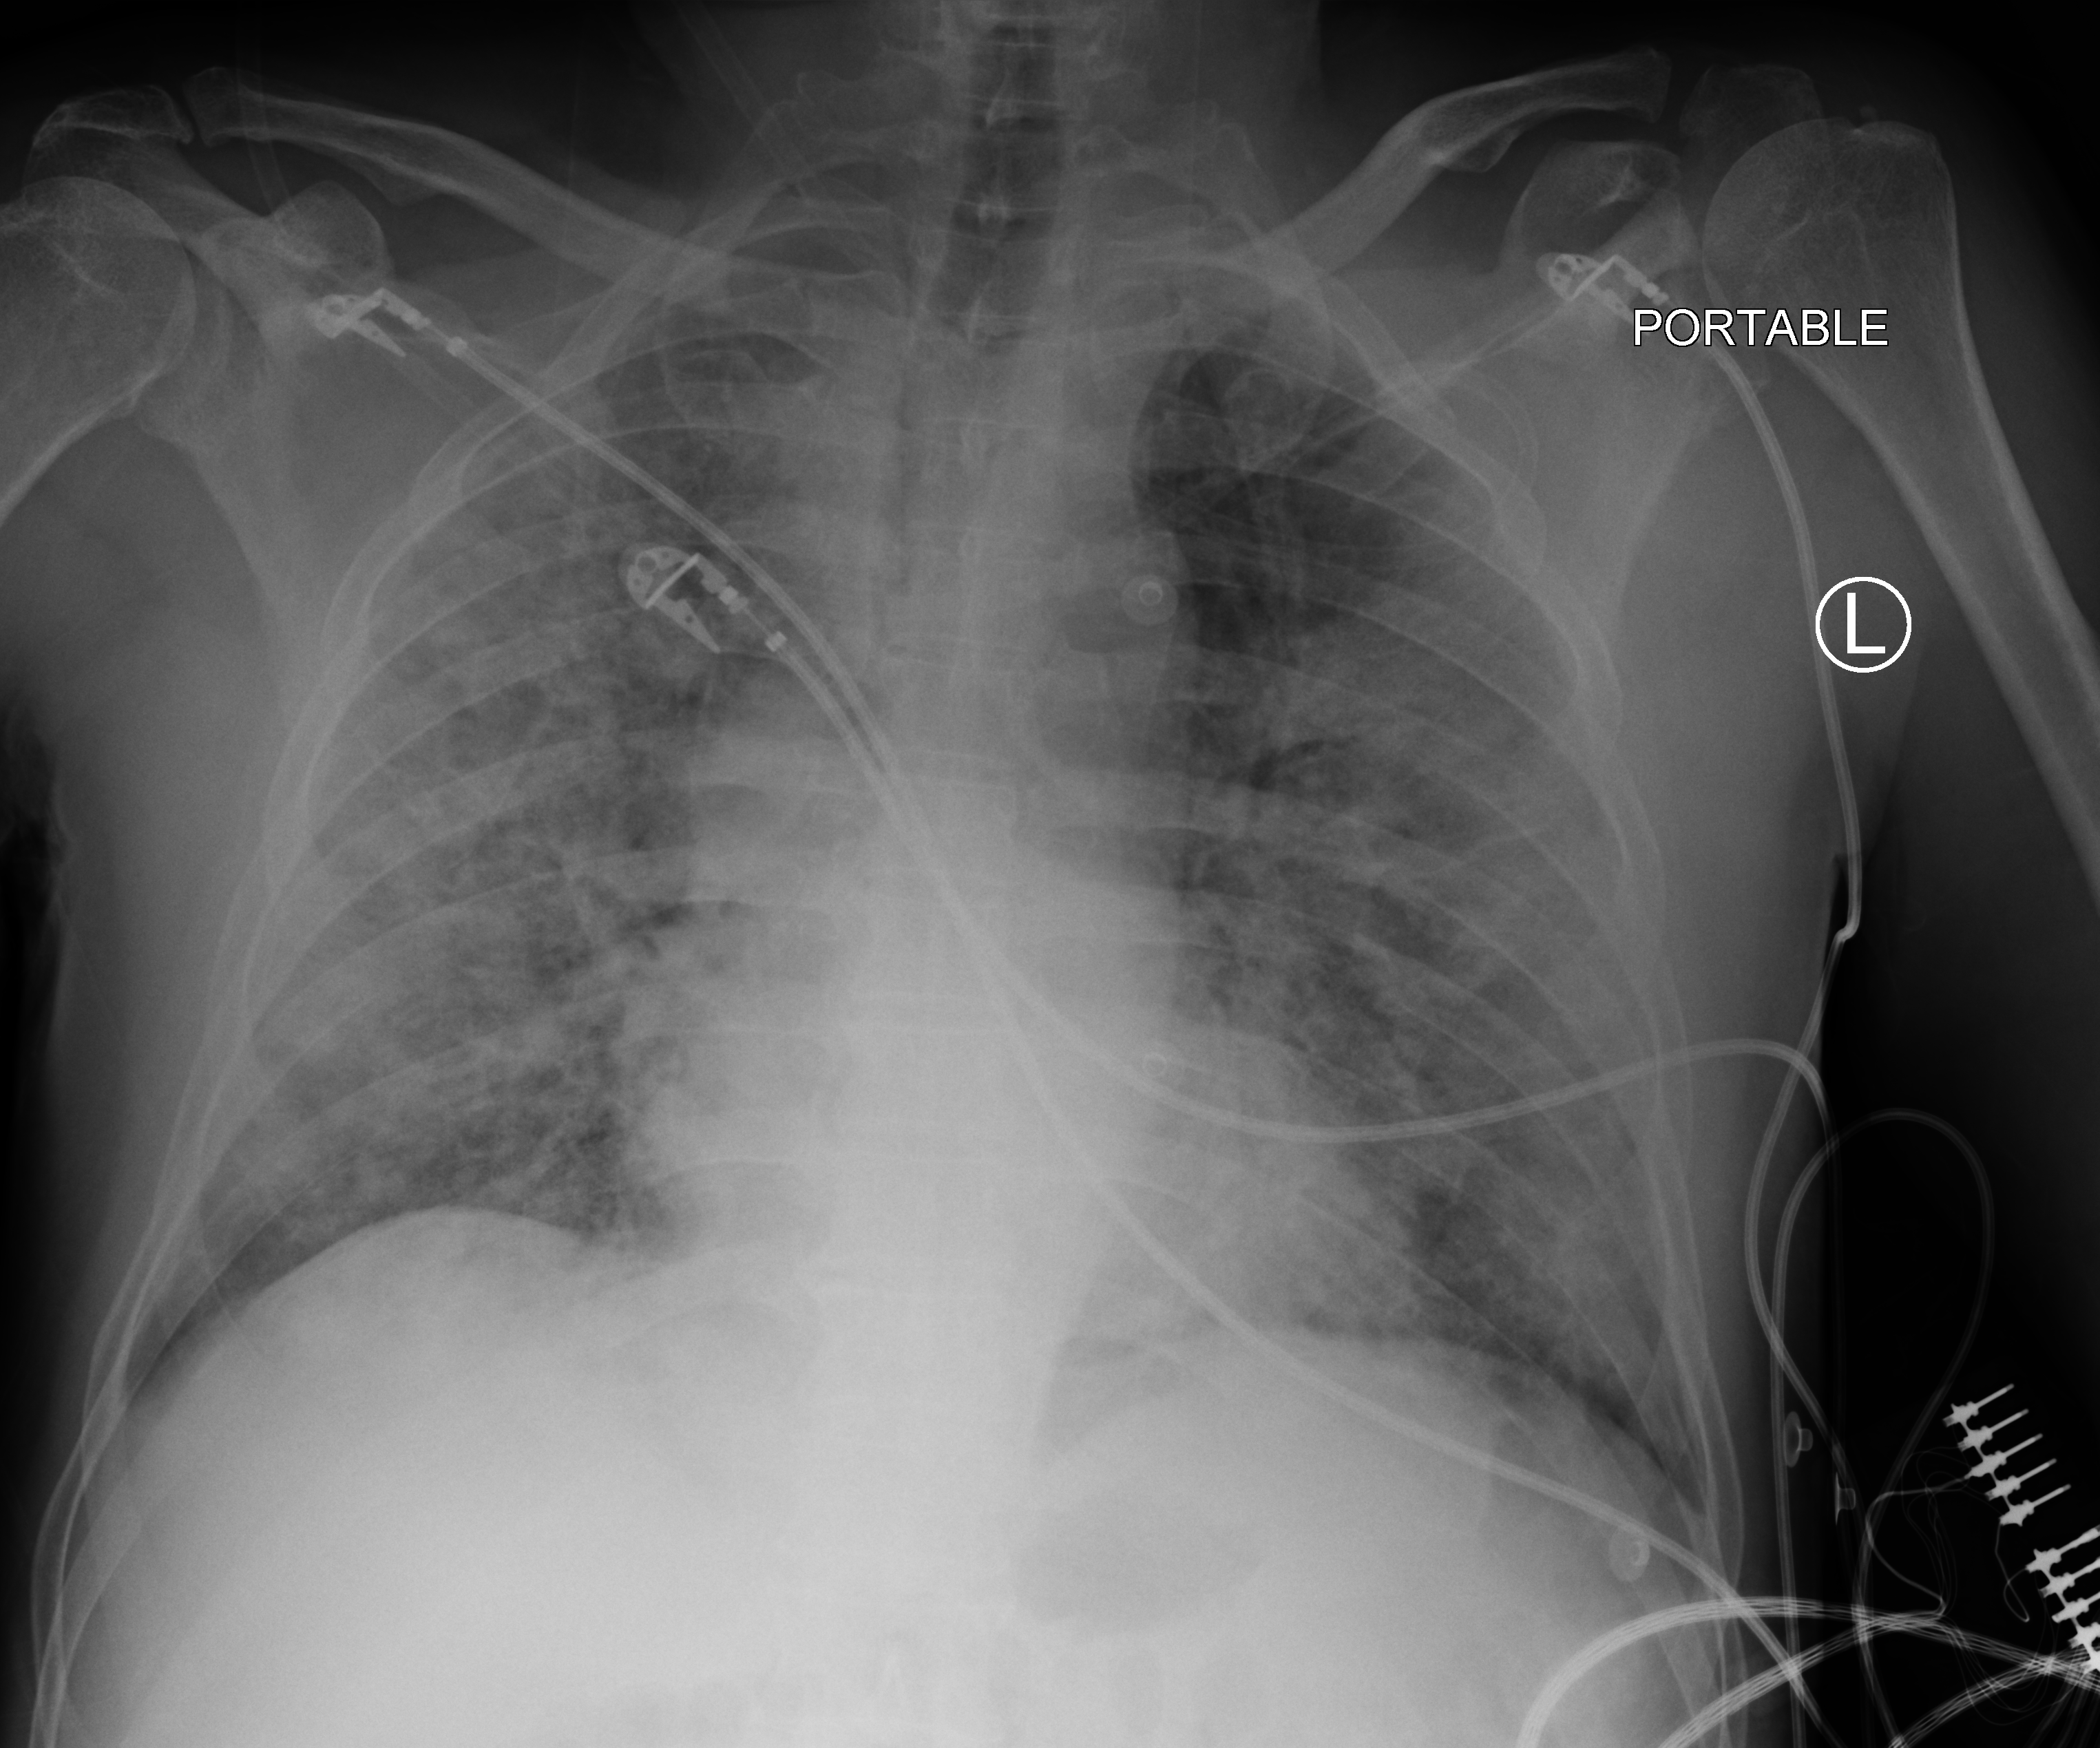
Chest X-ray (portable). Male patient hospitalised with COVID-19, age 60–74 years.
Hospital-stay facts (about this admission, not read from this image; timing relative to this image not recorded): length of hospital stay: 37 days; COPD (admission record): no.